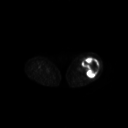
FDG PET of an extremity soft-tissue mass (from a PET/CT study), one axial slice. Slice 218 of 267 in the series (ordered by position). 3.27 mm slice thickness. 128 × 128 image matrix, field of view 700 × 700 mm. Female patient, age 62 years. Case-level facts recorded for this patient, not image findings: histological type: undifferentiated – high grade; grade: high; site of the primary tumour: left thigh.
Annotated regions visible in this slice (expert contour drawn on MRI and transferred to this co-registered scan by the dataset authors):
- gross tumour volume including surrounding oedema: bounding box [x1, y1, x2, y2] px = [82, 57, 100, 78]
- gross tumour volume (mass): [82, 57, 99, 78]